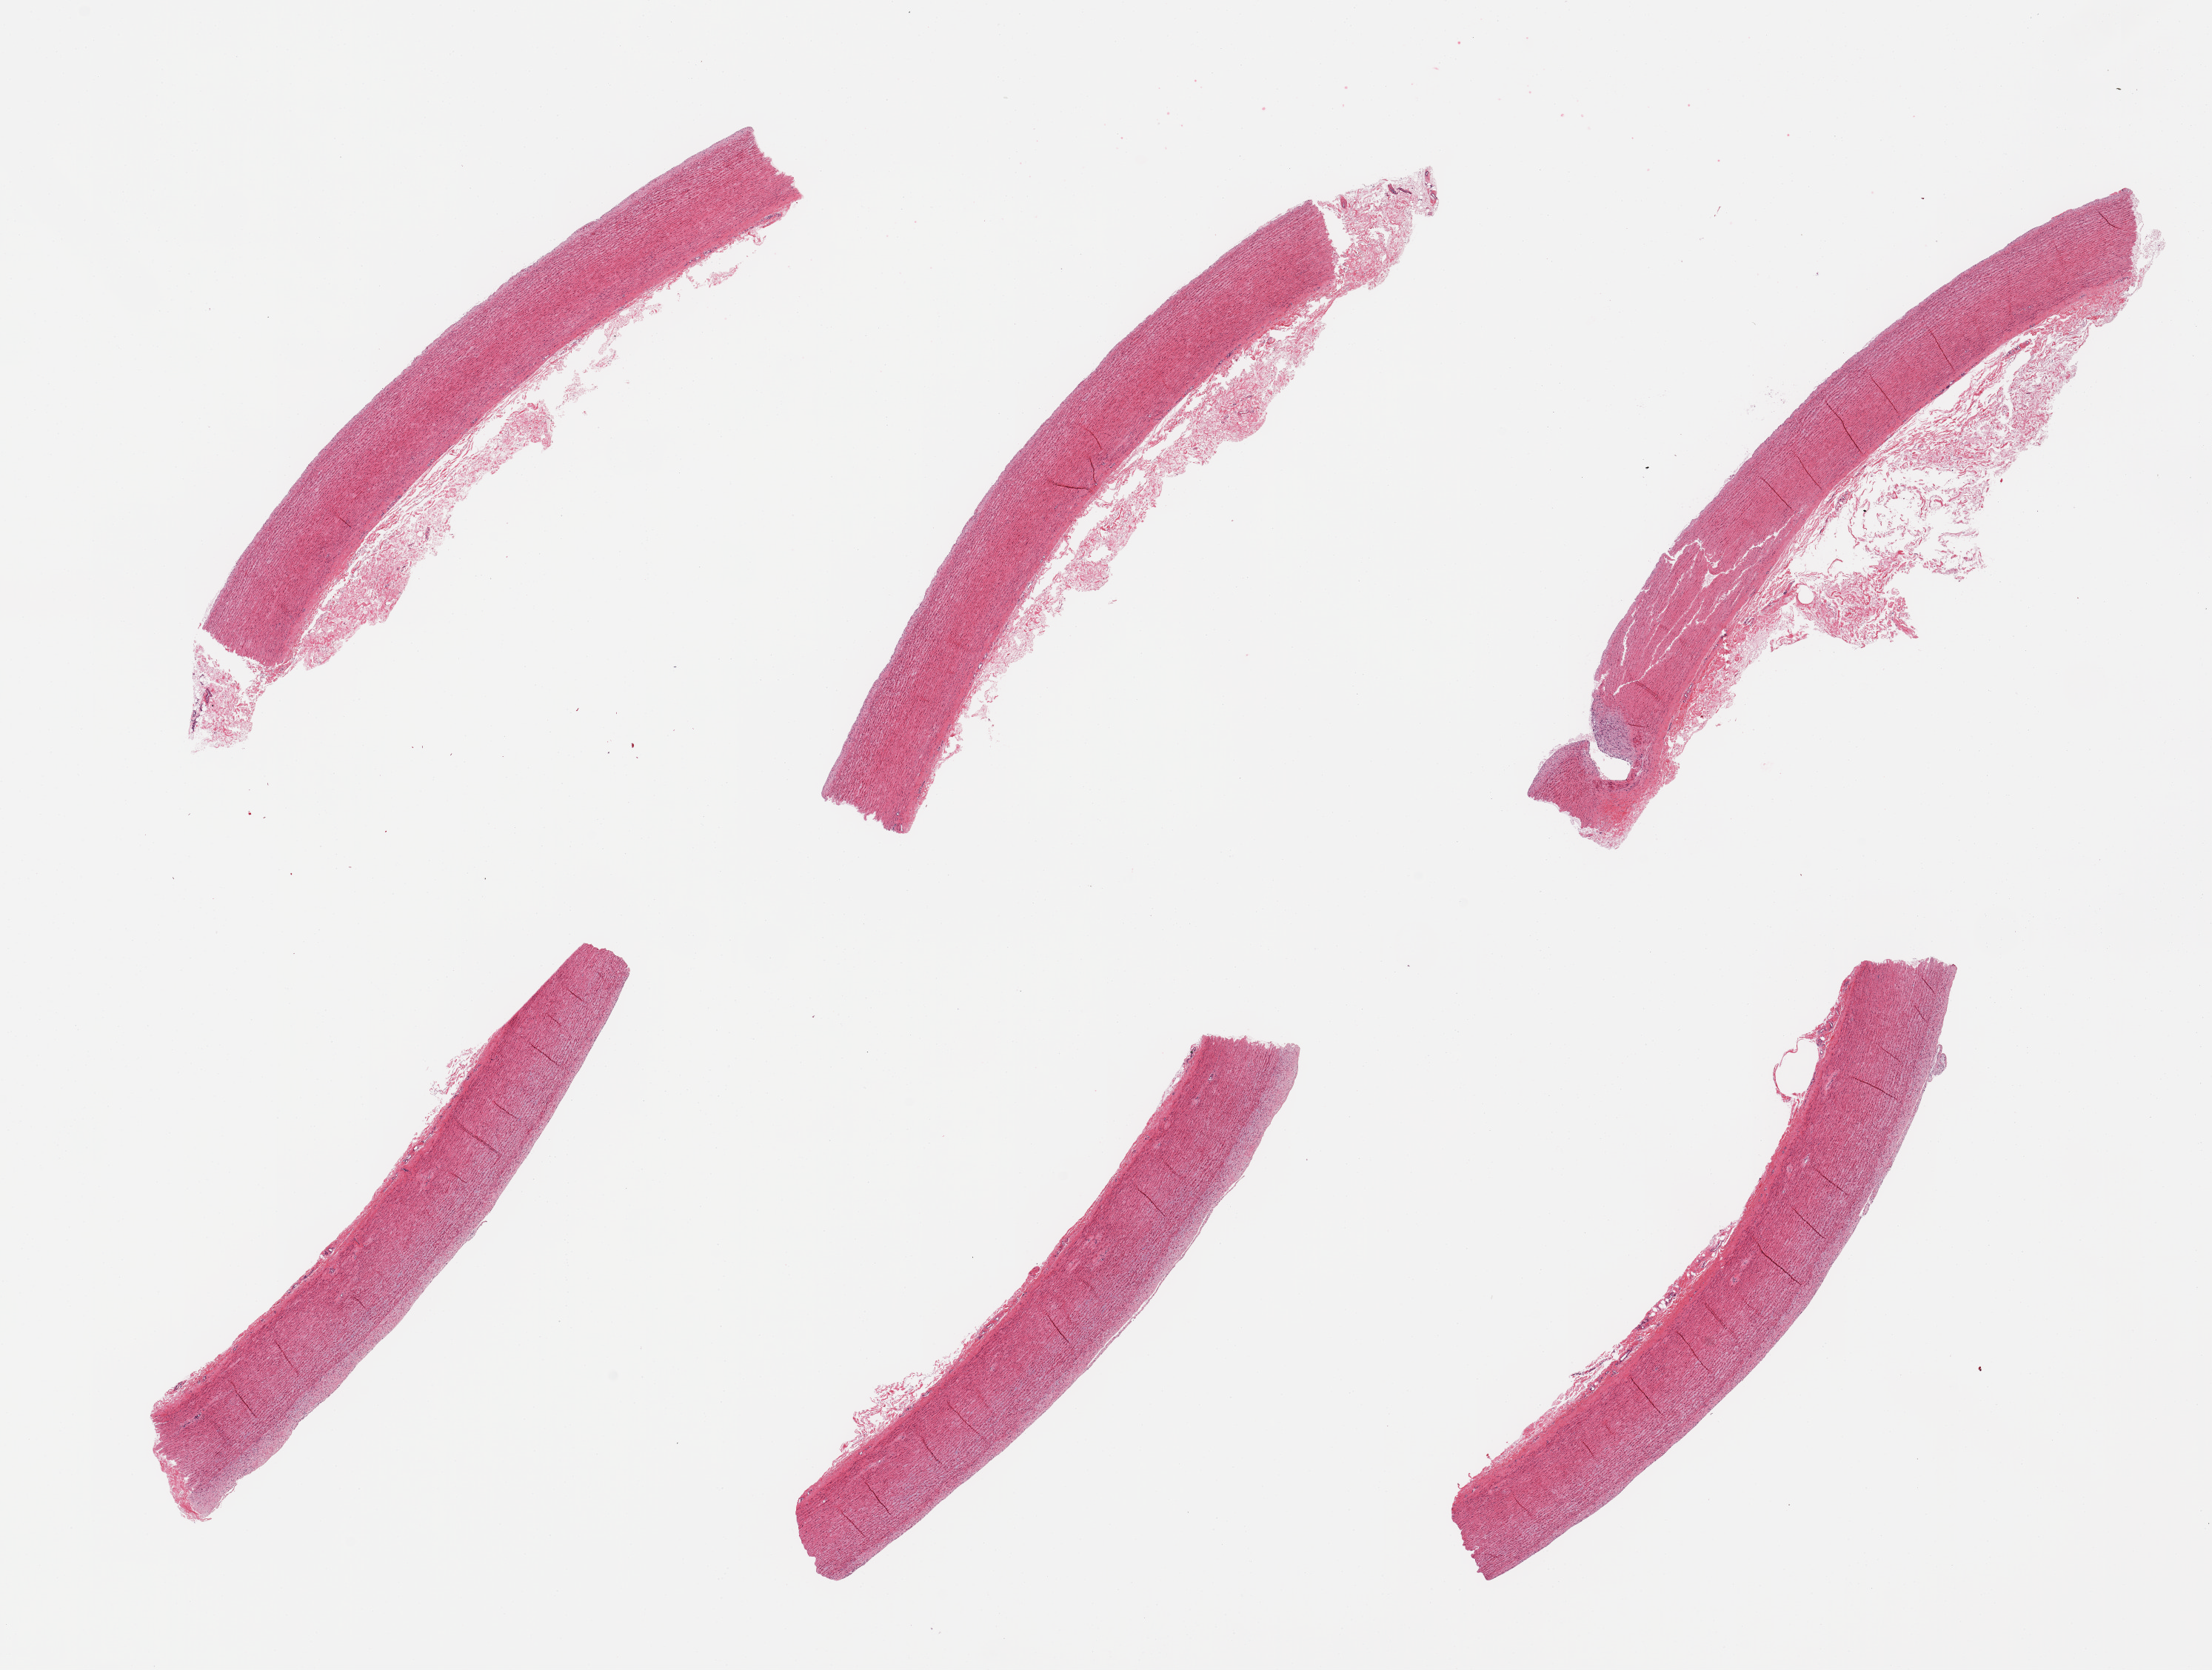
Digitized haematoxylin and eosin-stained section, a low-resolution overview of the entire scanned area, about 23.6 x 17.8 mm (acquisition: 20x scan). PAXgene-fixed, paraffin-embedded tissue. Sampled site (target tissue): aorta. Tissue donor sample. Male donor.
Review note (as recorded): 6 pieces; no lesions.